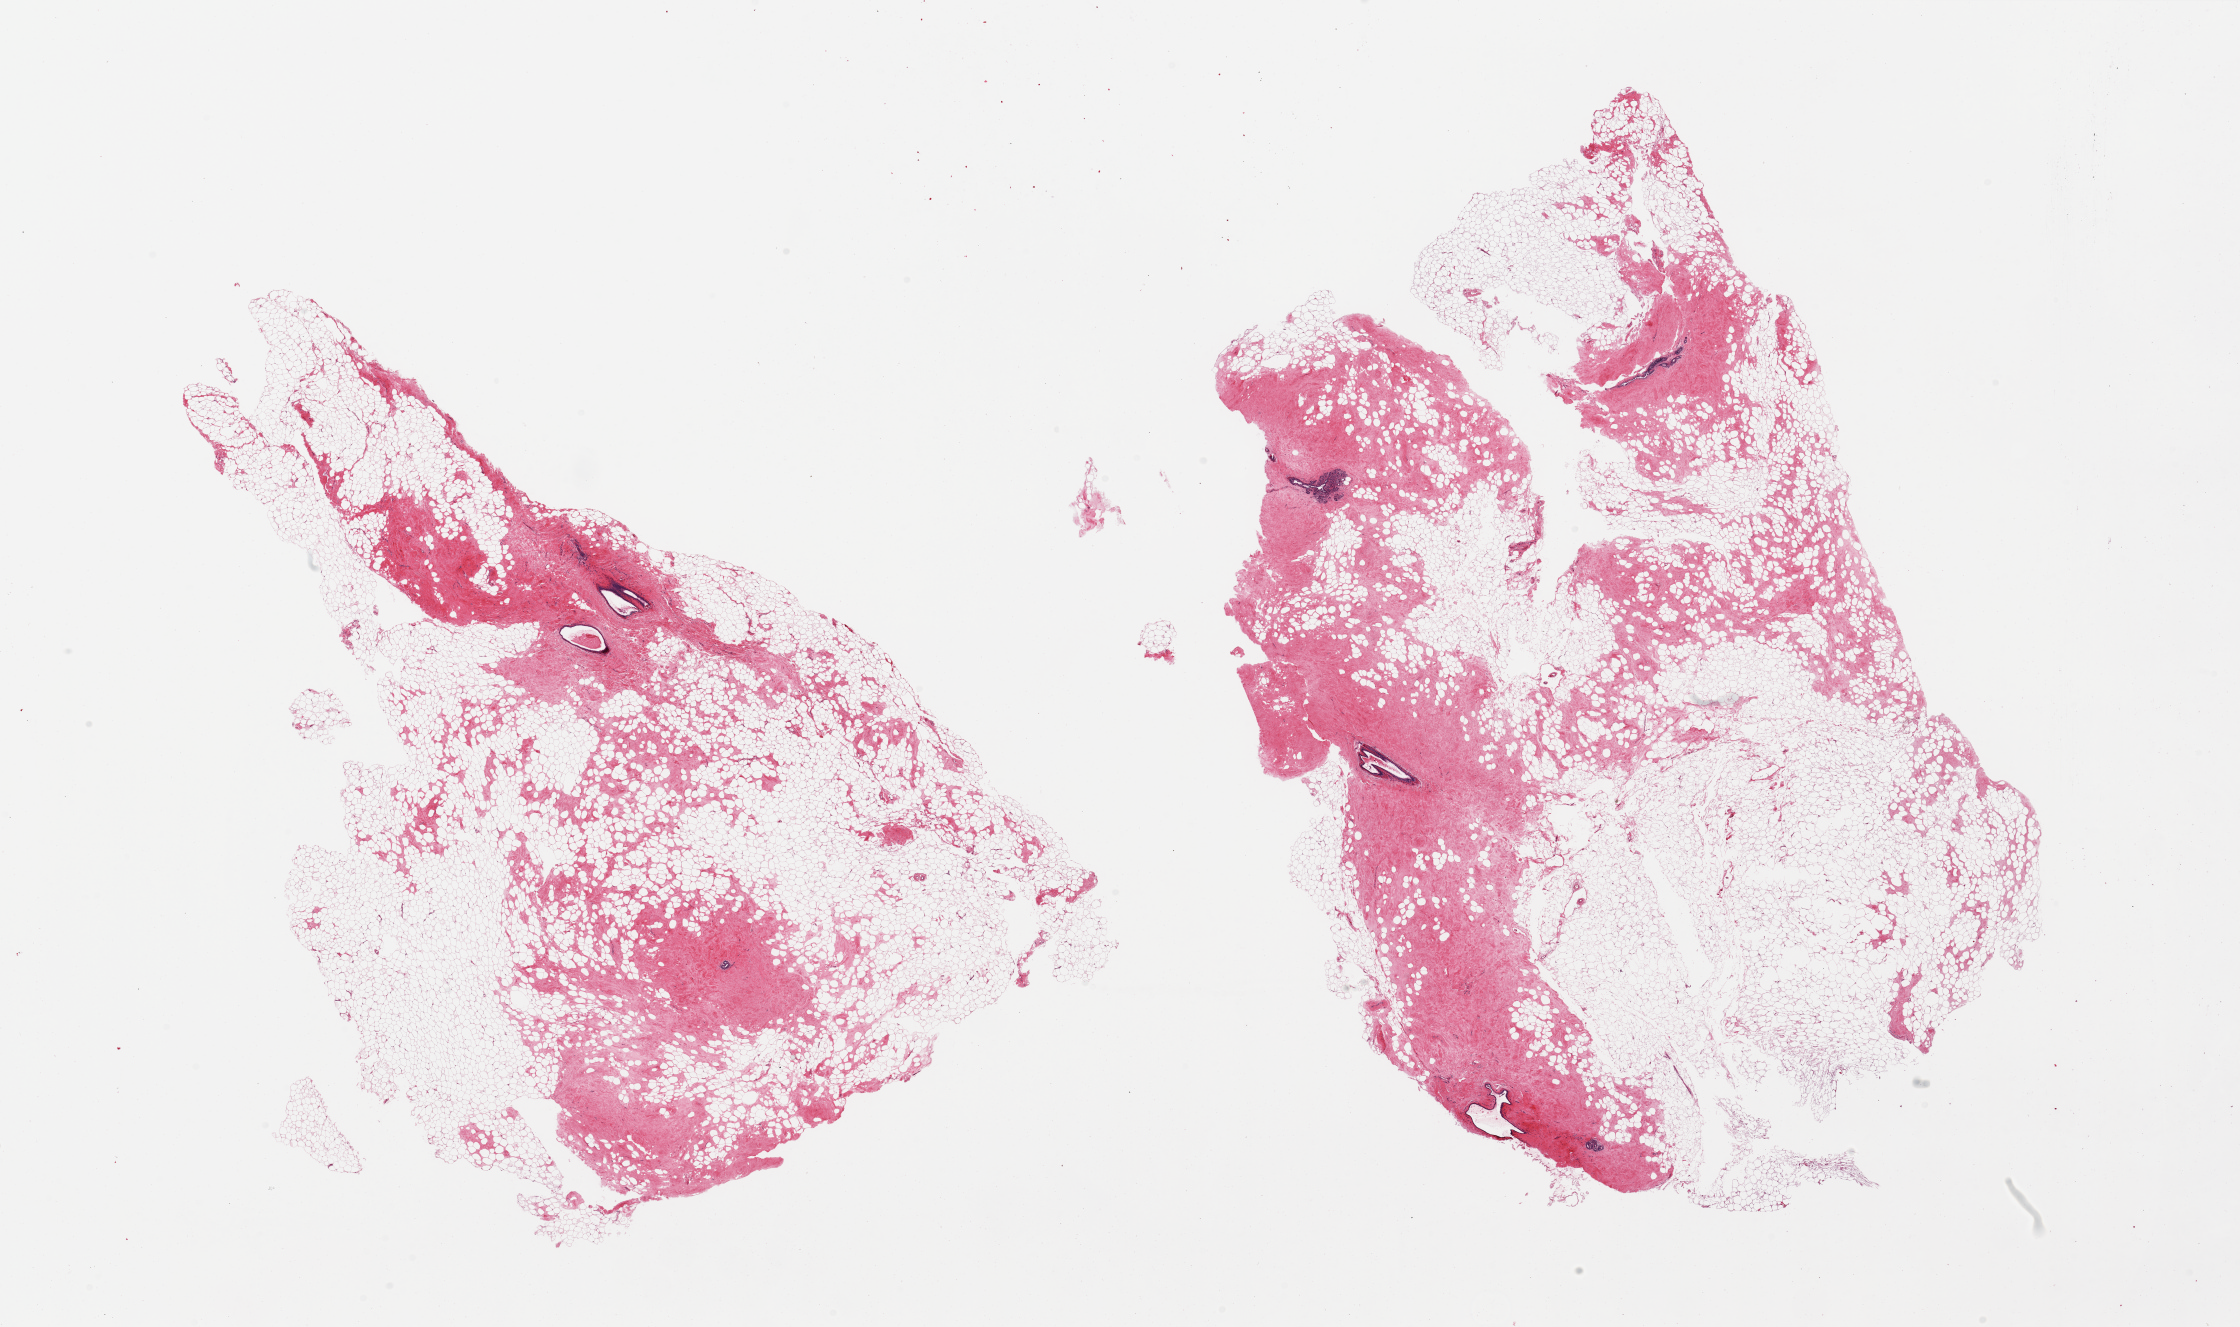
Haematoxylin and eosin whole-slide image — whole scanned area (about 35.4 x 21.0 mm) shown as a low-resolution overview, PAXgene-fixed paraffin-embedded (PFPE) section, section of breast (target tissue), donor tissue sample. Female donor.
- reviewer comment on this tissue sample: 2 pieces. Atrophic fibroadipose tissue with ducts & lobules. No sign of cancer or atypia